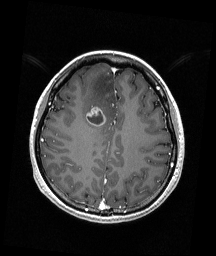
Brain MRI from a brain-tumour surgery series, one axial slice. Slice 63 of 192 in the series (ordered by position). T1-weighted post-contrast. 216 × 256 image matrix, field of view 211 × 250 mm. From the clinical record (not read from this slice): histopathology: Astrocytoma; WHO grade: 4; IDH mutation: yes.
Structures marked on this image (manually delineated by an expert):
- tumour: box from (x=86, y=106) to (x=106, y=126) px